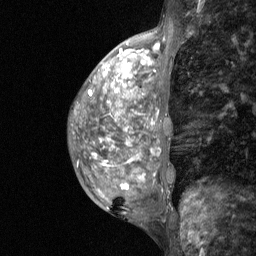
Breast MRI (dynamic contrast-enhanced), one sagittal slice; slice 22 of 64 in the series (ordered by position); dynamic contrast-enhanced study with each time point stored as its own series, time point 2 of 3 at this slice position (early post-contrast, ordered by acquisition time); 1.5 T; TE 4.8 ms, TR 27 ms; 2 mm slice thickness; 256 × 256 image matrix, field of view 200 × 200 mm. Female patient, age 36 years. Case-level facts recorded for this patient, not image findings: setting: breast cancer imaged before/during neoadjuvant chemotherapy; receptor status: HR-positive, HER2-negative.
Structures marked on this image (semi-automatic segmentation, software-assisted and operator-edited):
- analysis volume of interest (the breast-tissue region the enhancement analysis was run in; not a lesion): bounding box (x1, y1, x2, y2) in pixels: (73, 59, 174, 210)
- tumour enhancement mask (voxels above the 90 % enhancement threshold inside the analysis volume of interest): (116, 64, 132, 188)